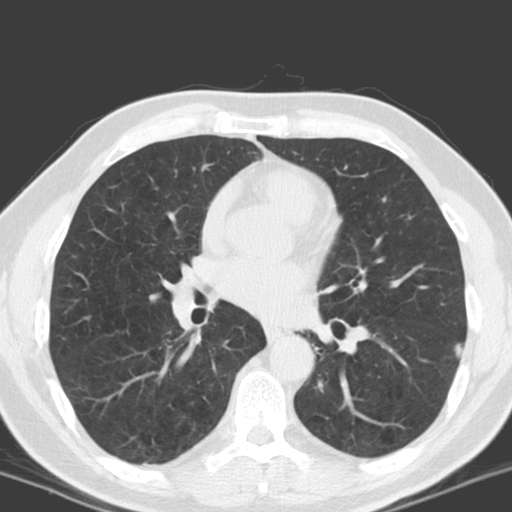
Chest CT (low-dose screening protocol), one axial image; baseline annual screen; lung window (W 1500 / L -600 HU); 3.2 mm slice thickness; standard (soft-tissue) reconstruction kernel (C); slice 92 of 158 in the series; 512 × 512 image matrix. Male participant, aged 57 years at enrolment. Former smoker at enrolment.
• Expert reader's lesion annotation, bounding box <439,332,477,365> (left, top, right, bottom; pixels).
• Reader record for this screening exam (exam-level; its link to the box is not recorded): non-calcified nodule or mass ≥4 mm, left lower lobe, 8 × 5 mm, poorly defined margins, ground glass attenuation.
• Official screen result: positive, change unspecified: nodule(s) >= 4 mm or enlarging nodule(s), mass(es), or other non-specific abnormalities suspicious for lung cancer.
• Later outcome: lung cancer diagnosed 816 days after this screen (after the third annual screen) — non-small cell carcinoma, left lower lobe, stage IV (AJCC 6th edition), 13 mm at pathology.